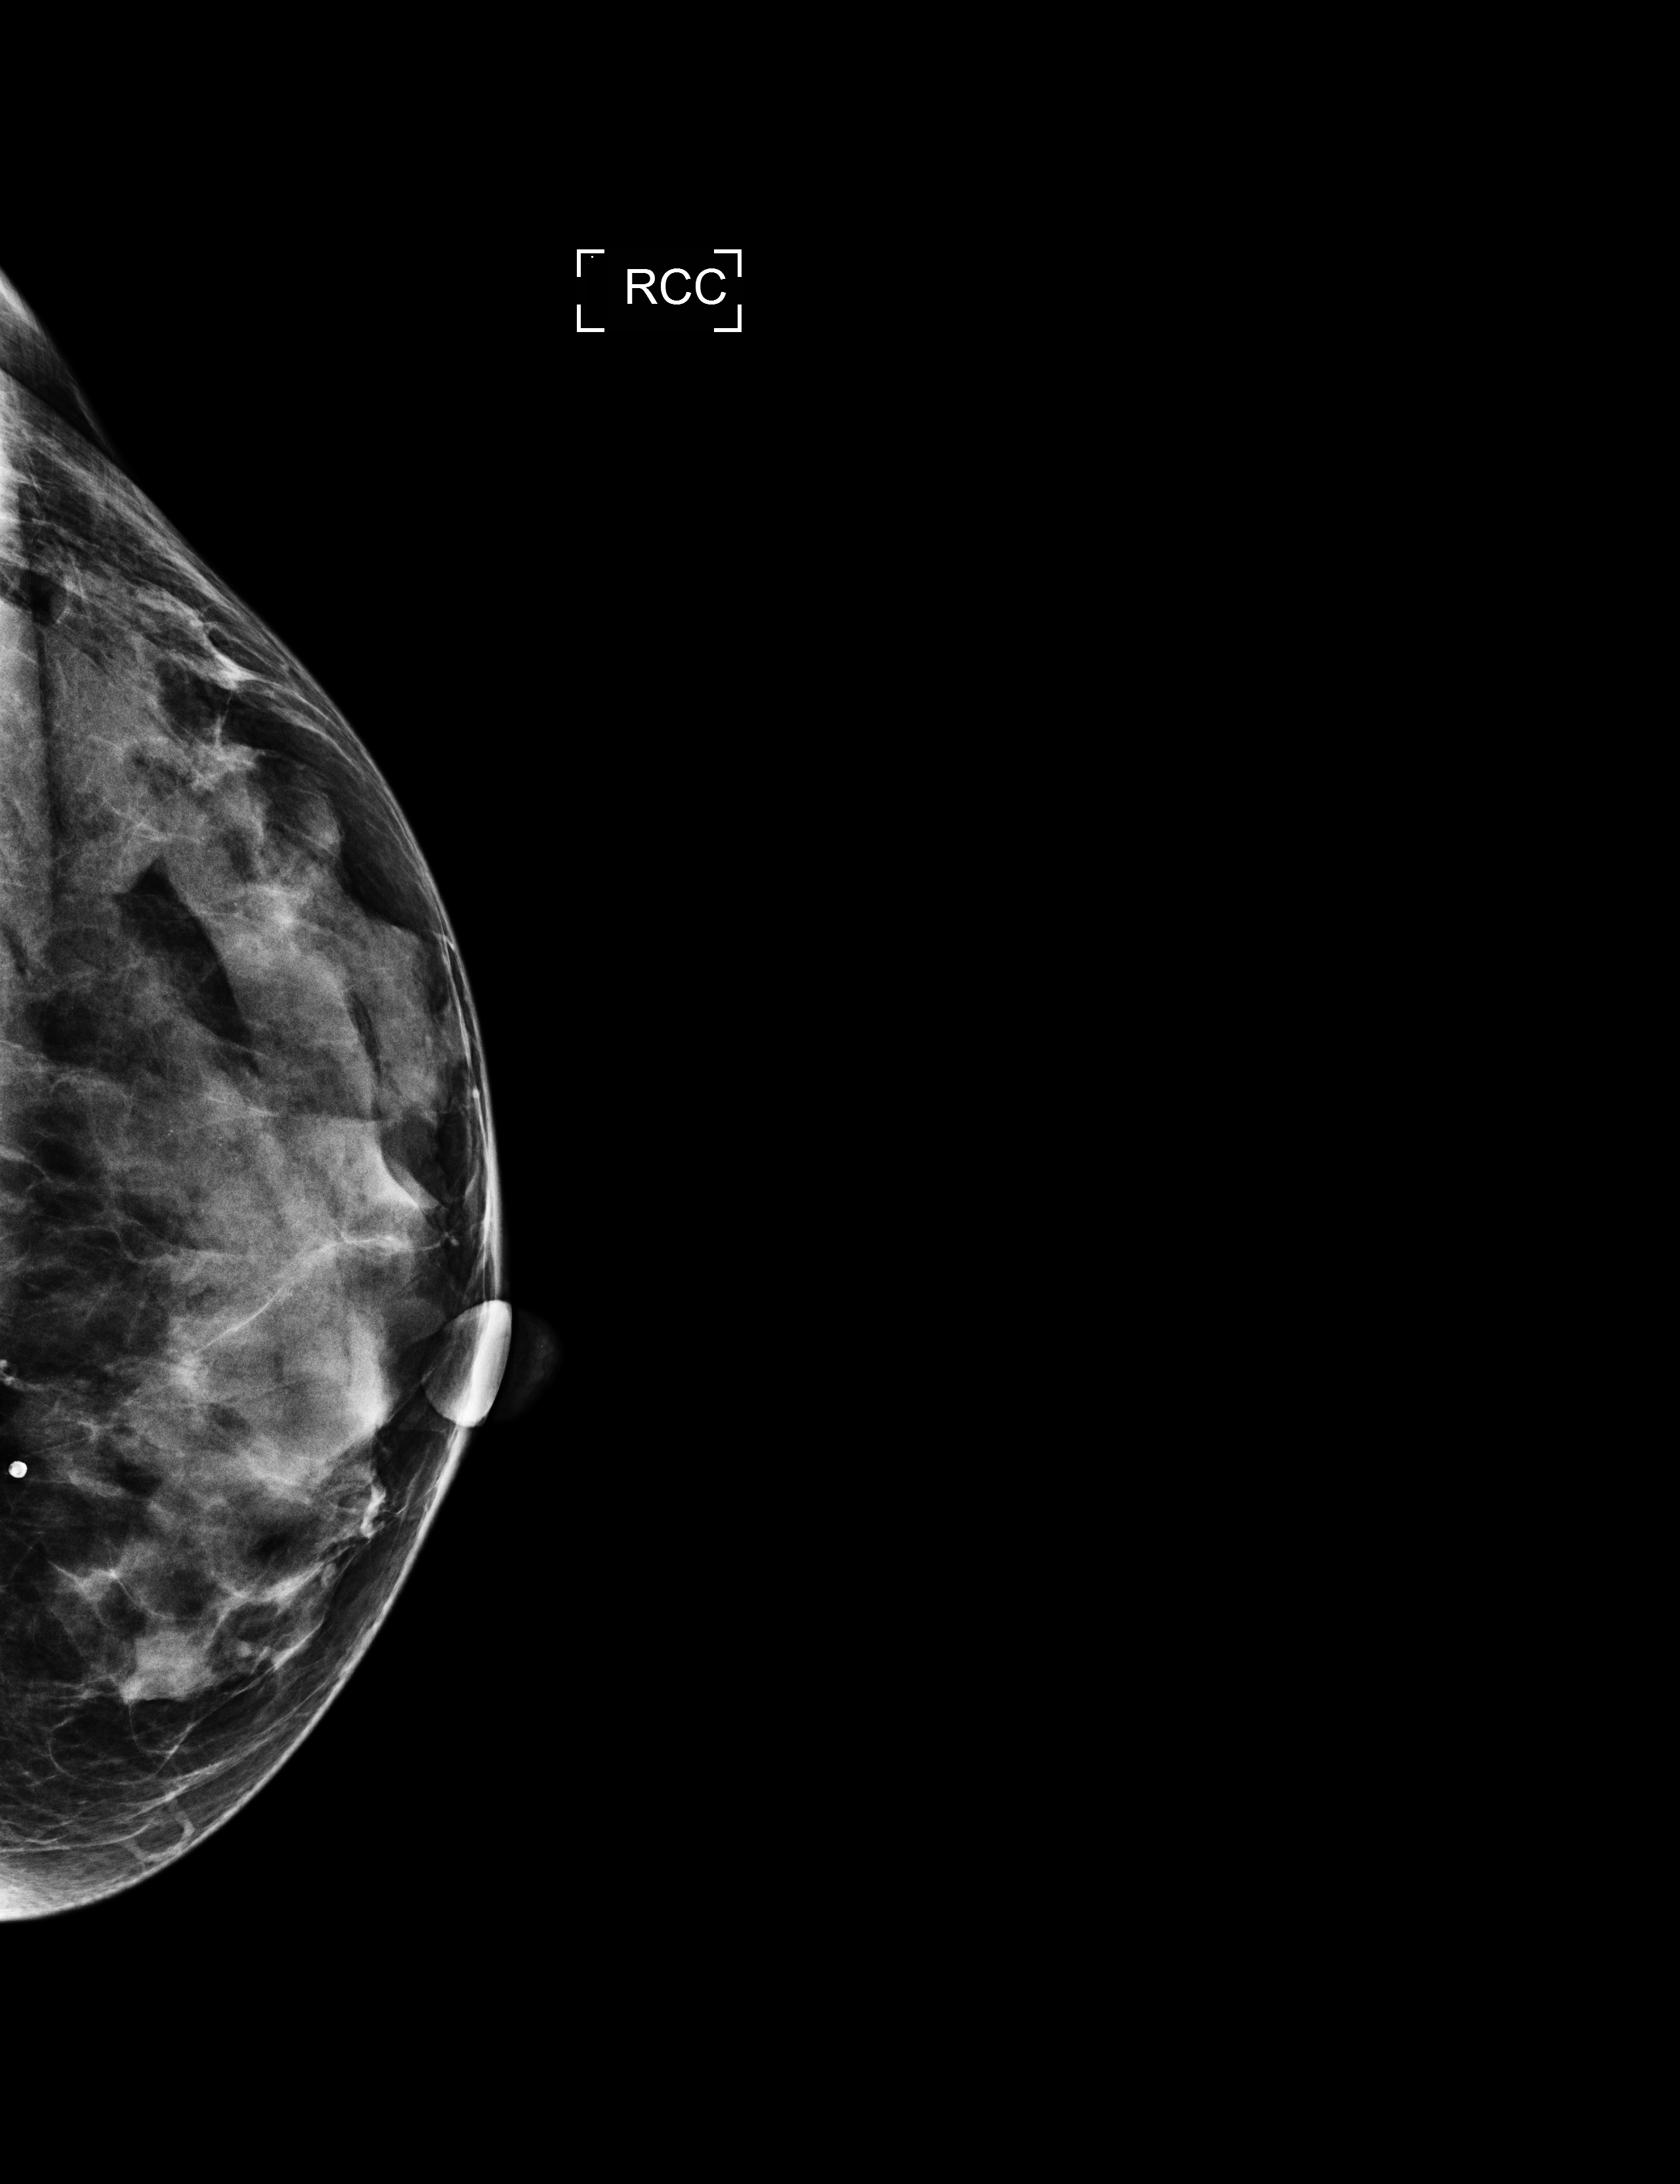
Annual screening mammography examination, compressed breast thickness 23 mm, system: Selenia Dimensions. Female patient, age 54 years.
Image type: full-field digital mammogram. Breast: right. Projection: CC view.